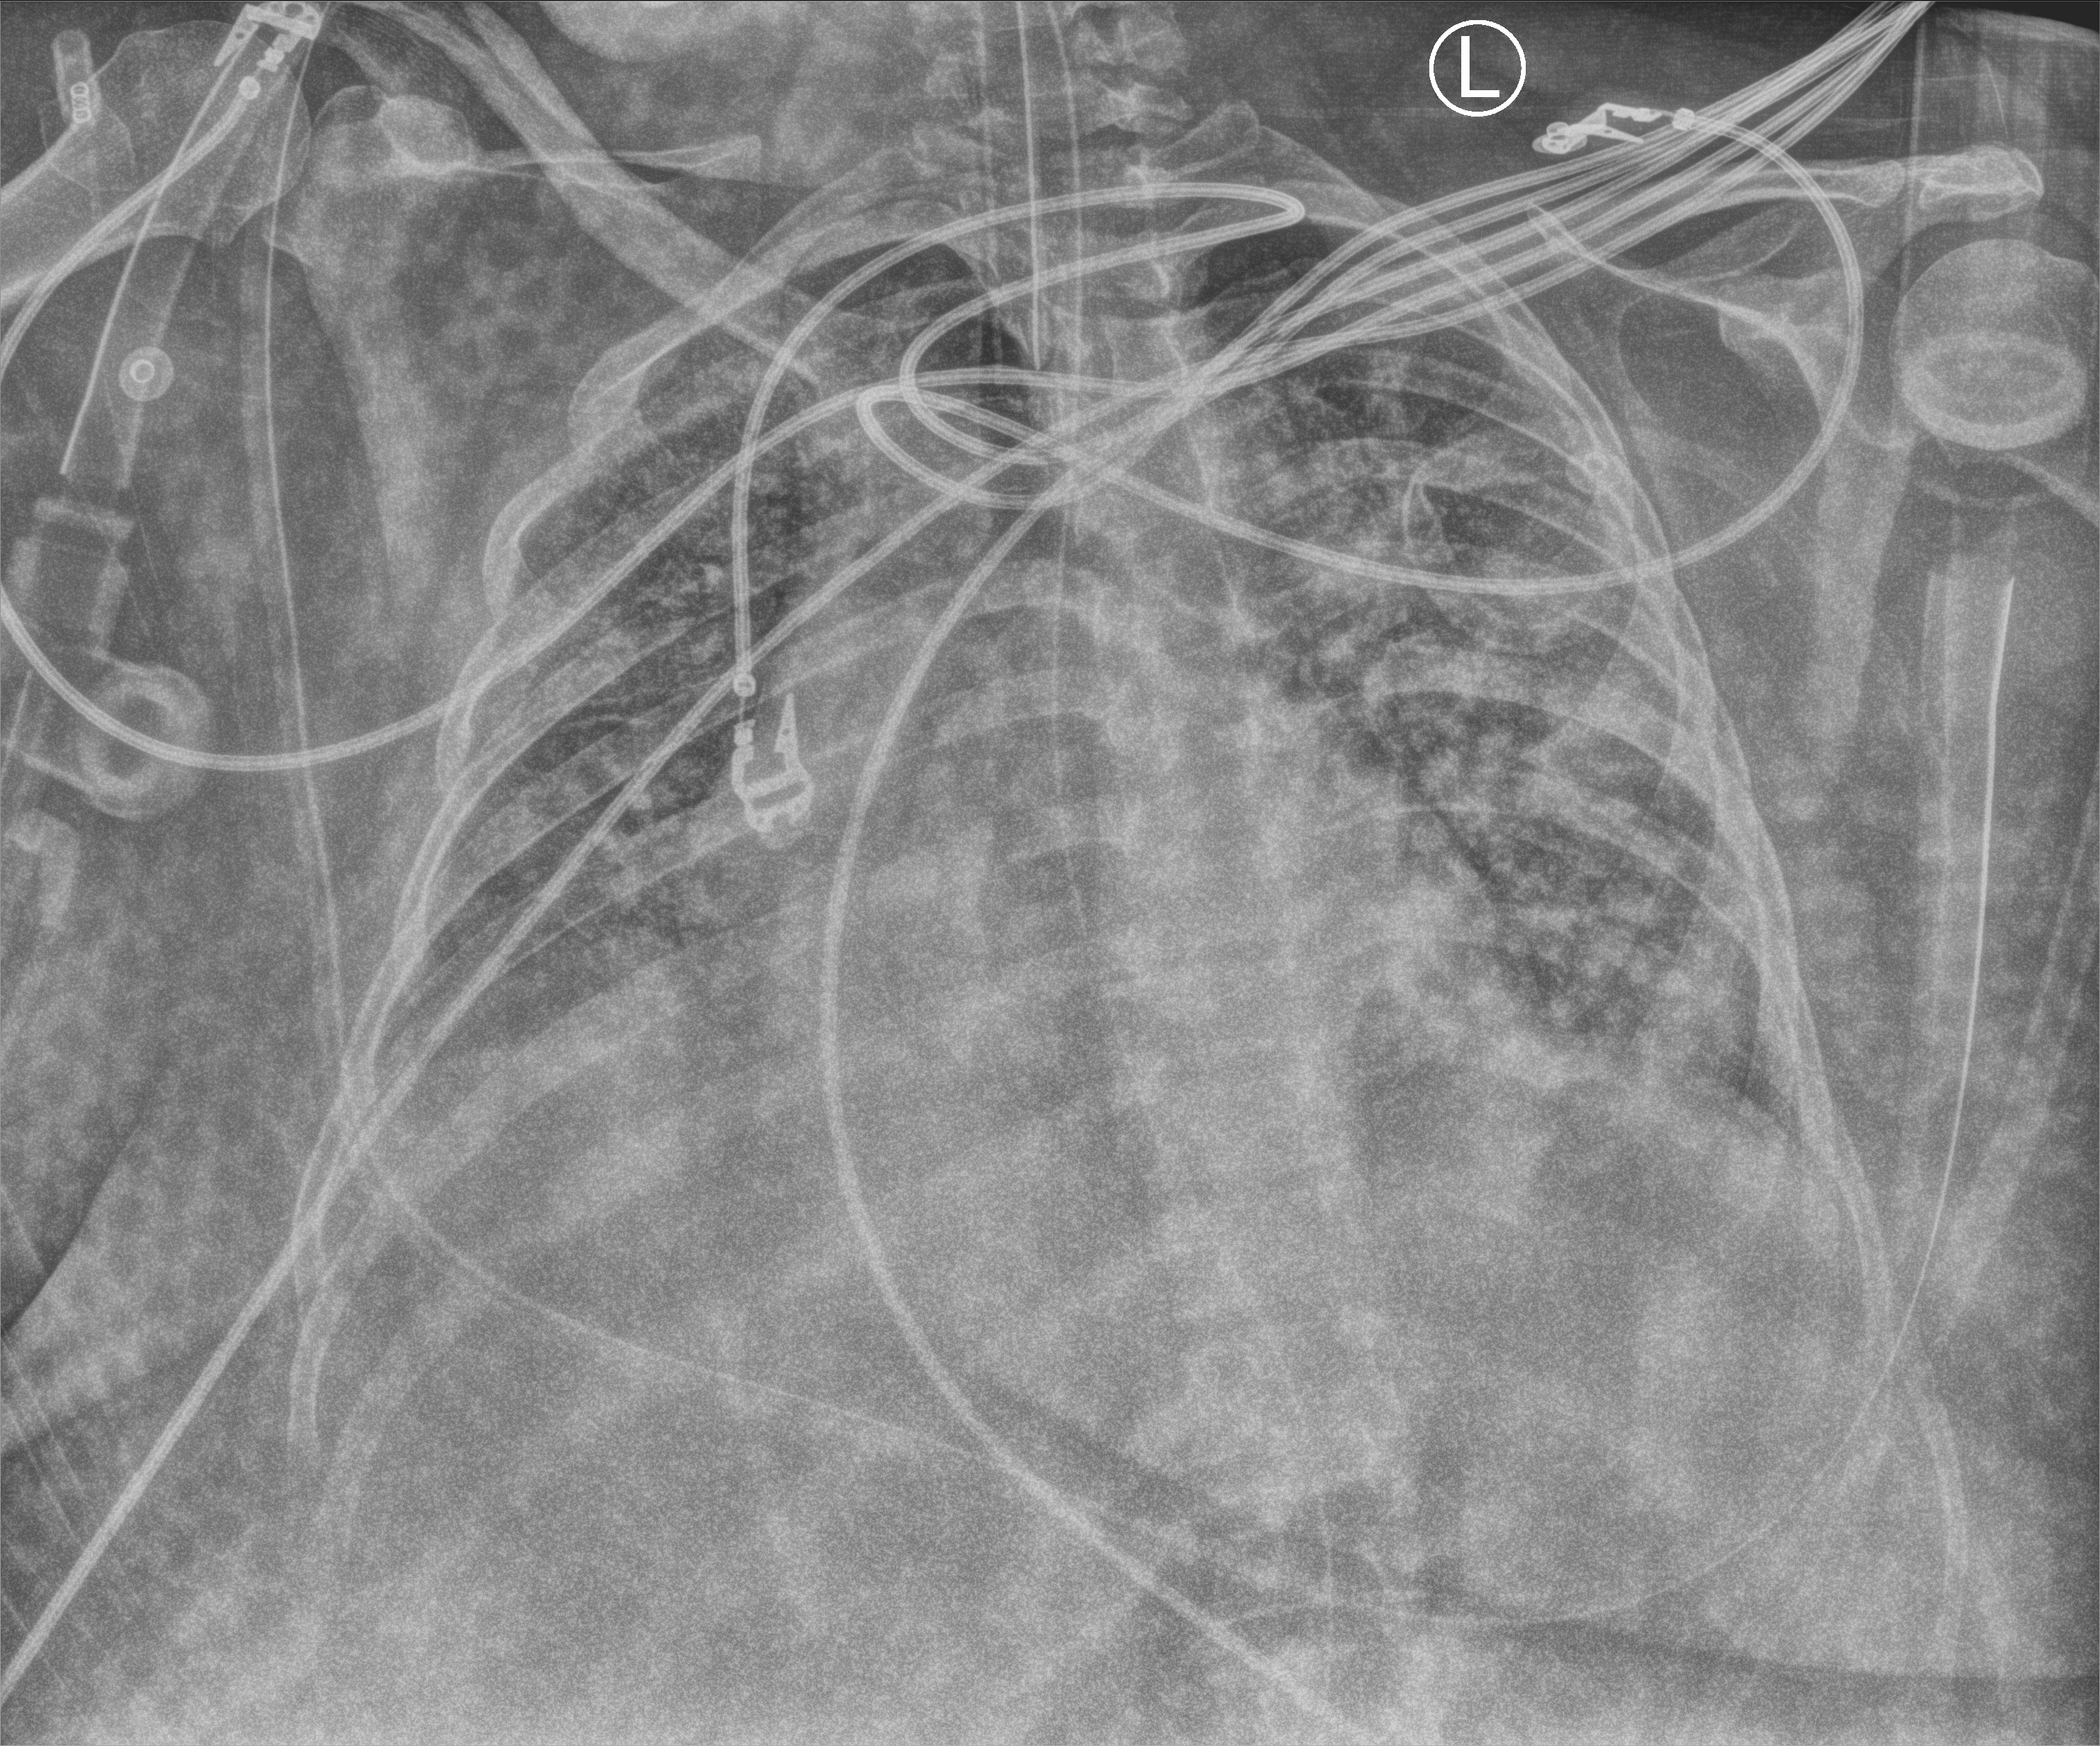
Bedside chest radiograph (computed radiography), anteroposterior (AP) projection. Female patient hospitalised with COVID-19, age 18–59 years.
Hospital-stay facts (about this admission, not read from this image; timing relative to this image not recorded):
- admitted to intensive care during this hospital stay: yes
- length of hospital stay: 23 days